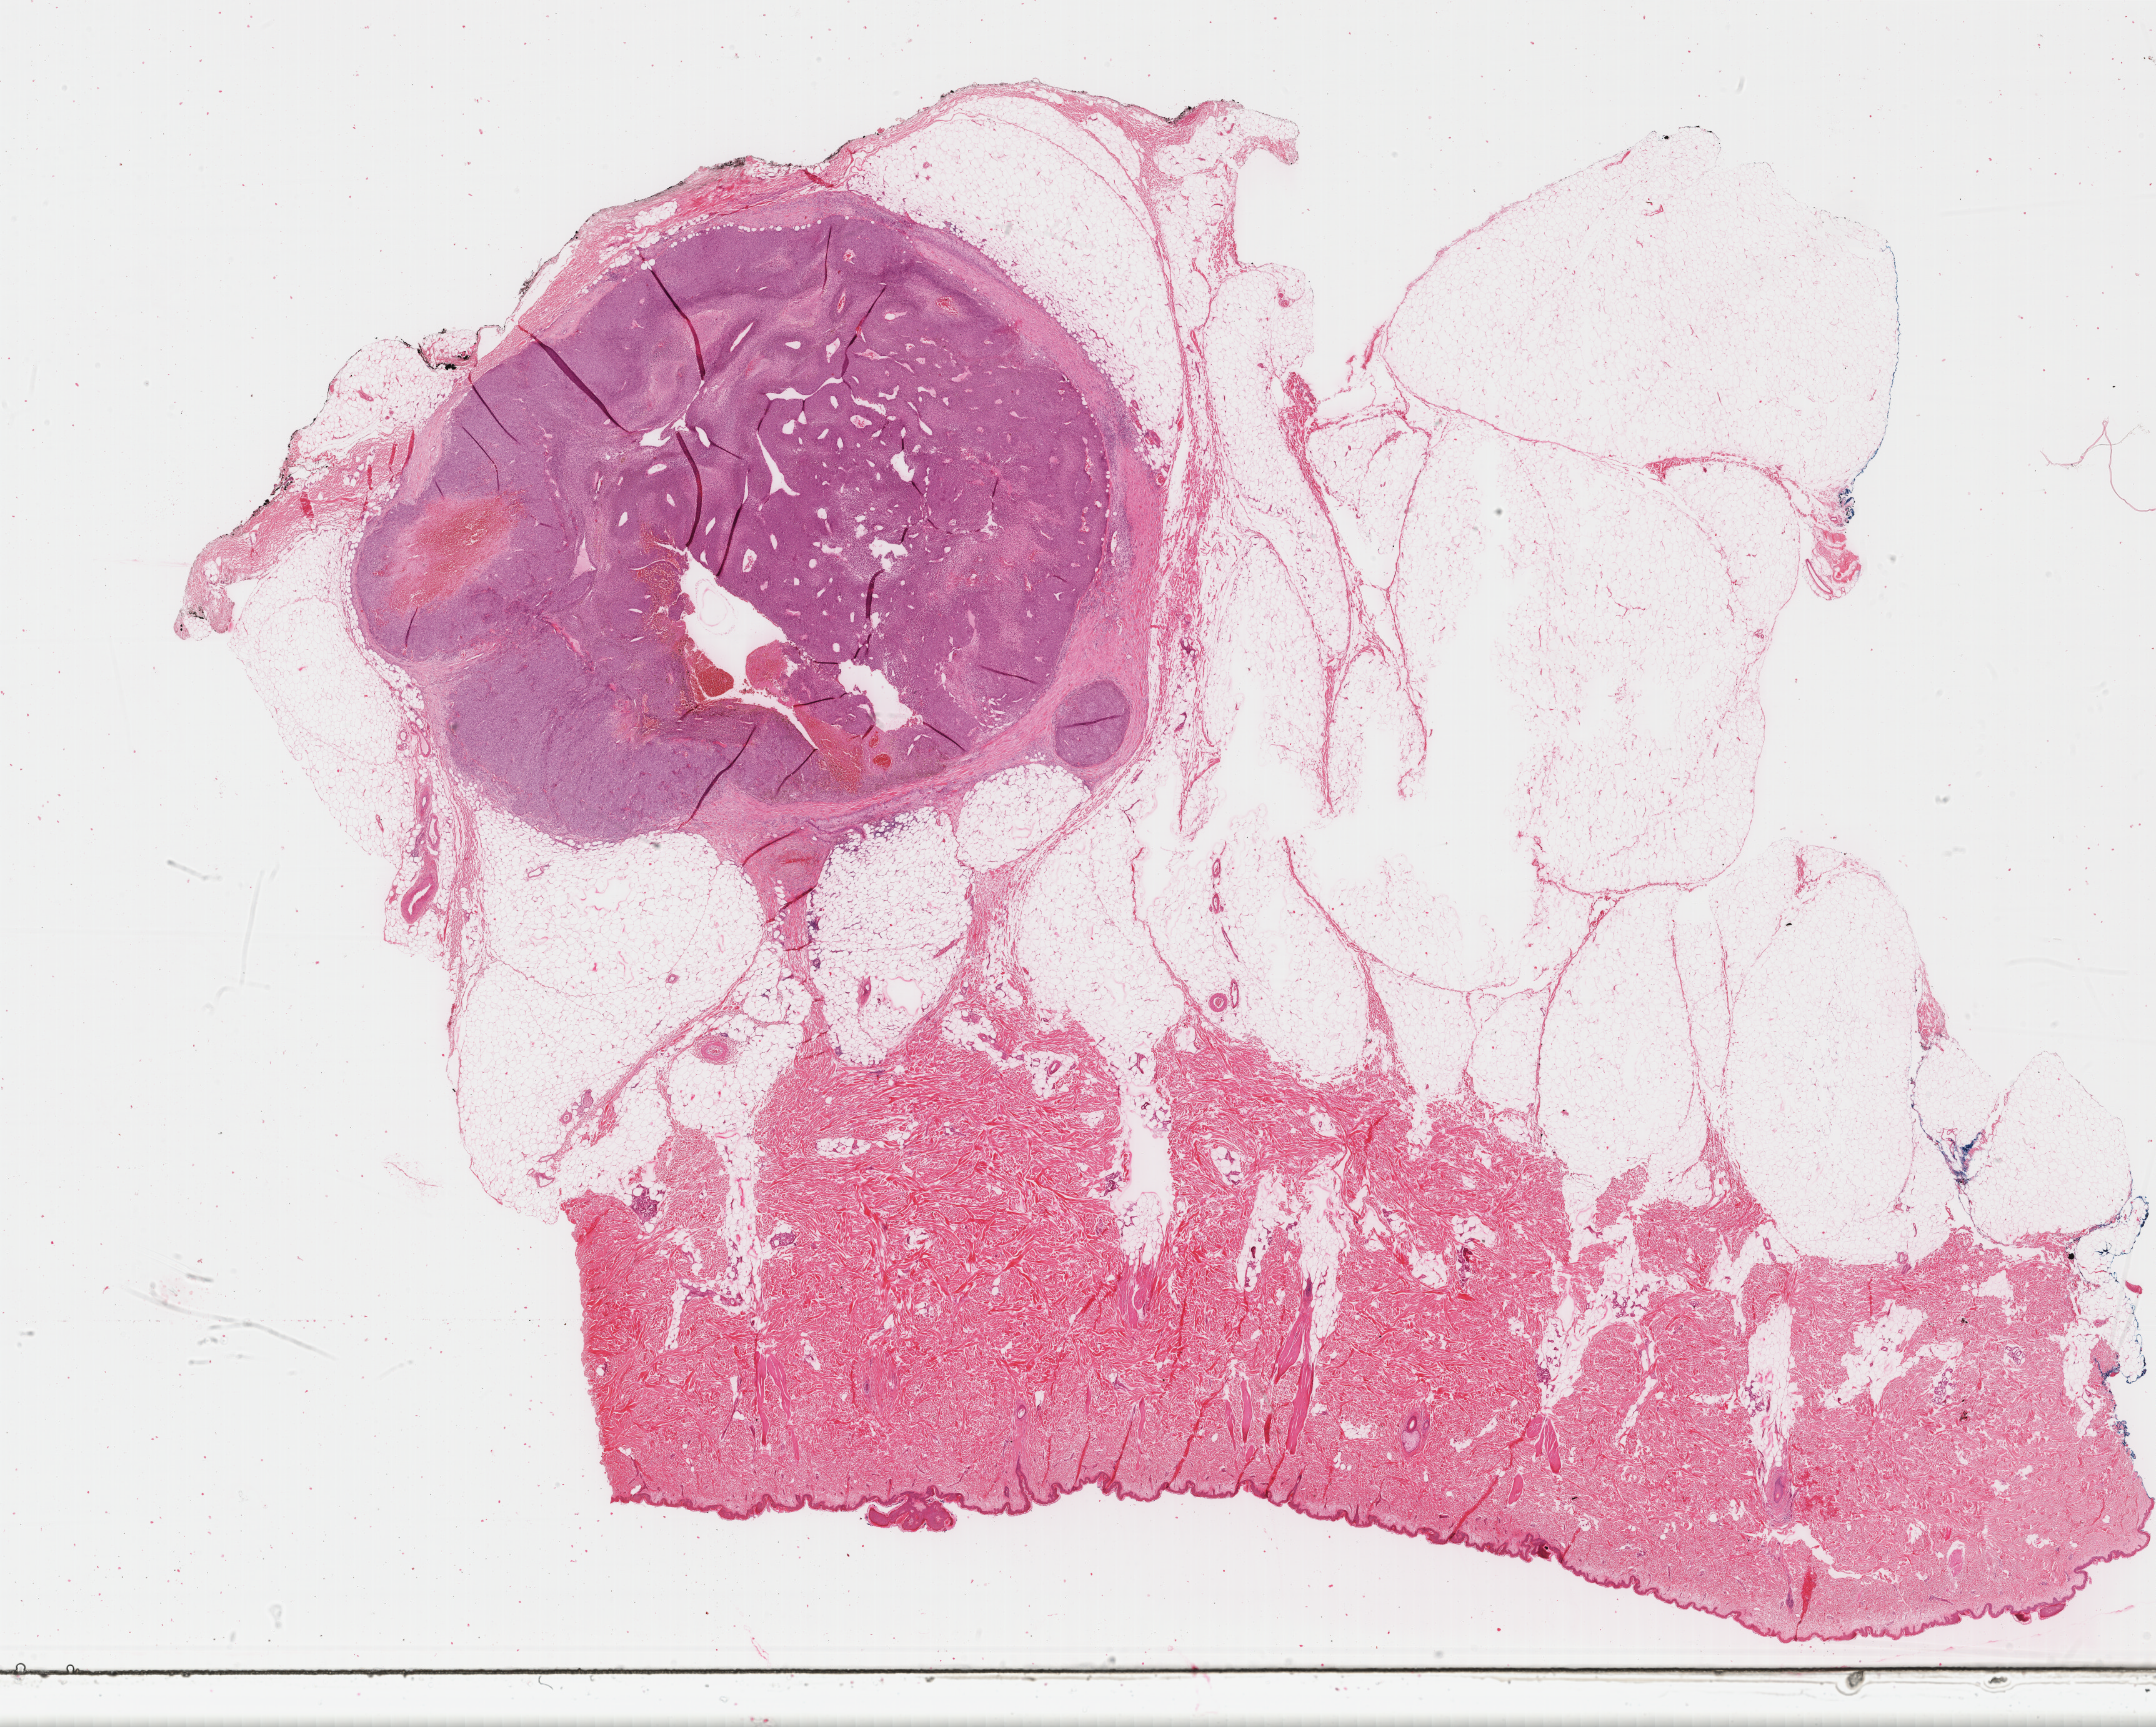
Digitized Hematoxylin and eosin (H&E) stained tissue section (whole slide), low-resolution overview of the scanned area, about 27.4 x 21.9 mm (acquisition: 40x scan). FFPE section. Skin, primary tumour sample. Male, age 67 years at initial diagnosis.
Histologic diagnosis: Malignant melanoma, NOS.